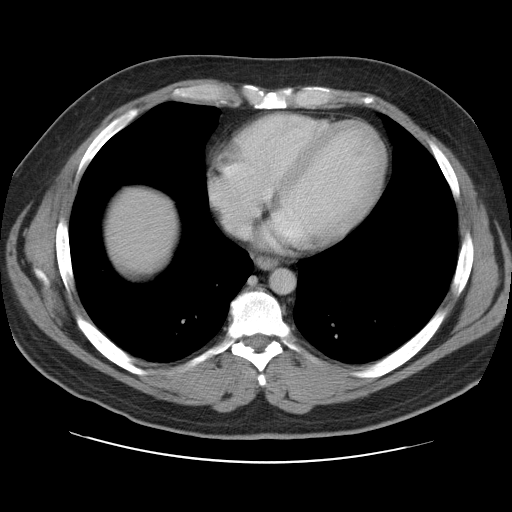
Contrast-enhanced abdominal CT, one axial slice; position 105 of 109 along the scan axis; intravenous contrast given; soft-tissue window (W 400 / L 40 HU); 5 mm slice thickness; 512 × 512 image matrix. Male patient, age 35 years. Case-level facts recorded for this patient, not image findings: diagnosis: colorectal cancer liver metastases, imaged before liver resection; multiple liver metastases: yes; largest metastasis: 2.8 cm; chemotherapy before resection: yes.
Outlined on this slice (manually delineated by an expert):
- liver: bounding box <105,187,177,275> (left, top, right, bottom; pixels)
- planned liver remnant (the part of the liver to remain after resection): <105,187,176,275>